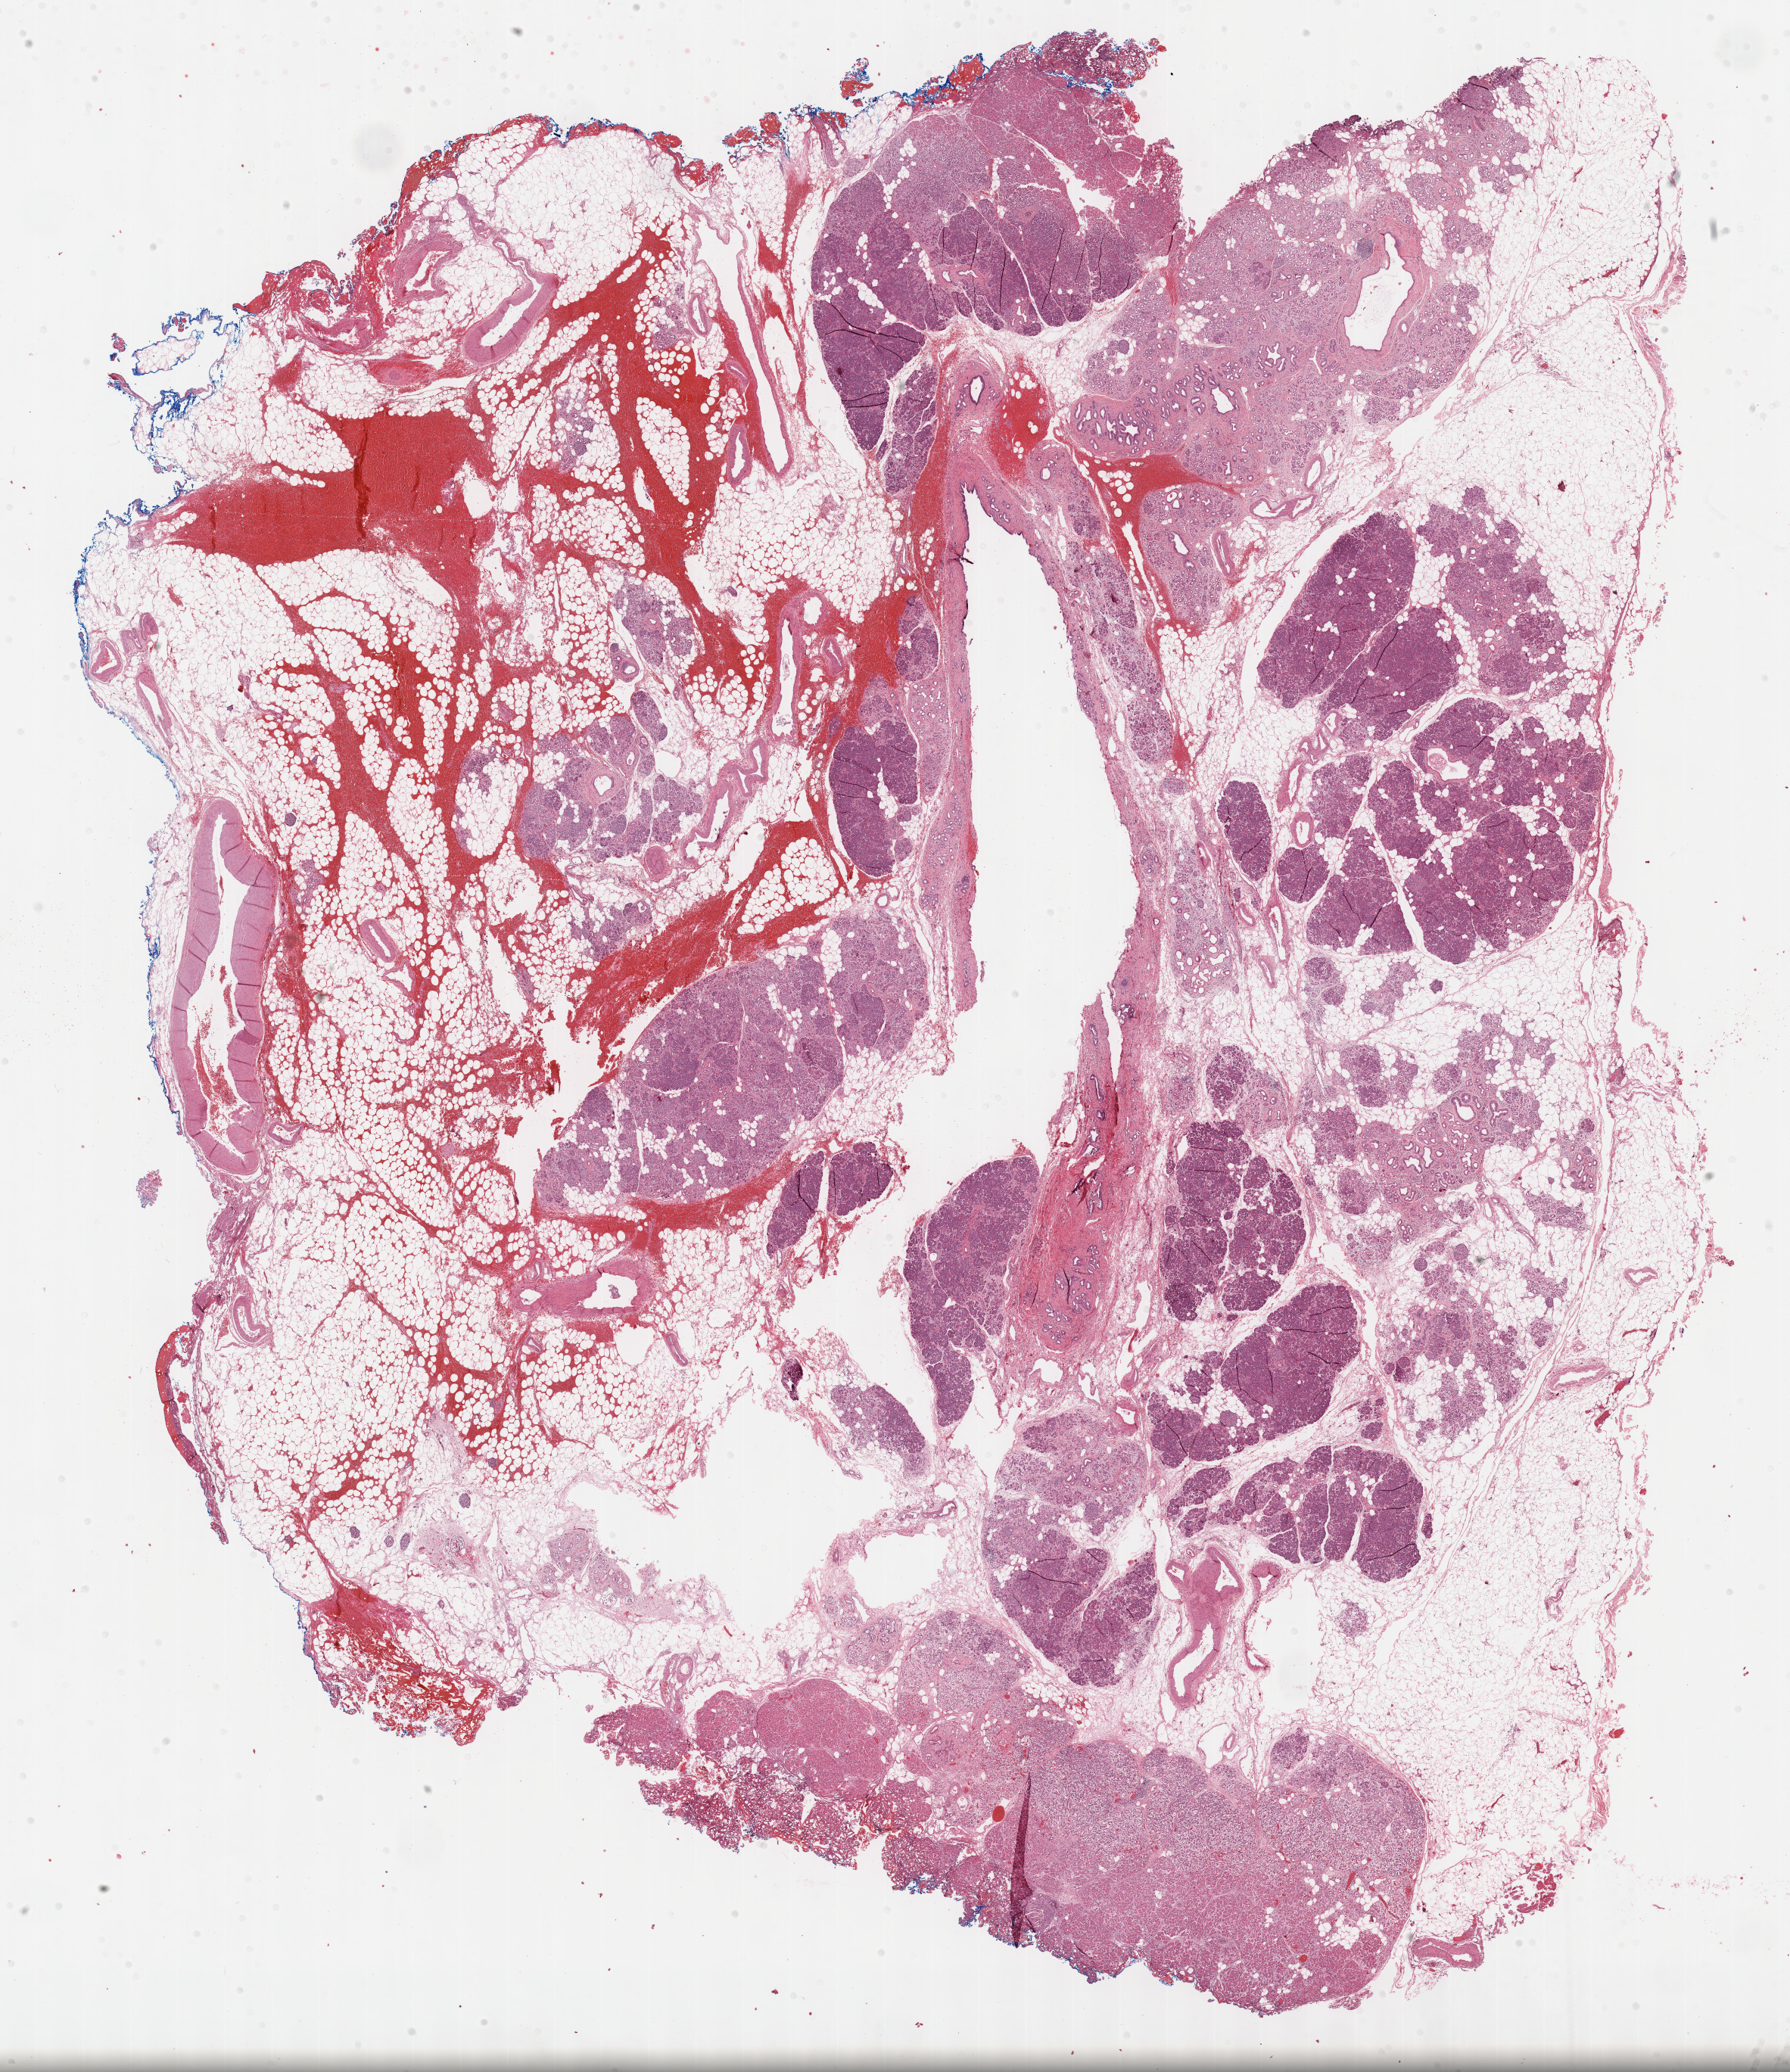
Whole-slide histology image, H&E-stained, low-resolution overview of the scanned area, about 19.1 x 22.1 mm; FFPE section; sample: primary tumour, pancreas. Patient: male, age at initial diagnosis 81 years. Histologic grade: G2 (moderately differentiated).
* diagnosis: Infiltrating duct carcinoma, NOS (head of pancreas)
* lymph nodes positive (case pathology): 0 of 5 examined
* AJCC pathologic stage: IIA (6th edition)